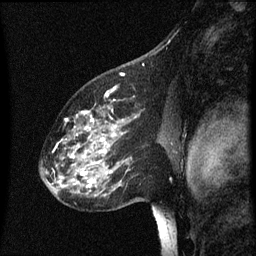
Breast MRI (dynamic contrast-enhanced), one sagittal slice. Position 41 of 60 along the scan axis. Dynamic contrast-enhanced series, image 2 of 3 at this slice position (ordered by acquisition). 1.5 T. TE 4.2 ms, TR 8 ms. 2 mm slice thickness. 256 × 256 image matrix, field of view 200 × 200 mm. Female patient, age 60 years.
Annotated regions visible in this slice (semi-automatic segmentation, software-assisted and operator-edited):
- analysis volume of interest (the breast-tissue region the enhancement analysis was run in; not a lesion): bounding box <49,96,142,197> (left, top, right, bottom; pixels)
- tumour enhancement mask (voxels above the 70 % enhancement threshold inside the analysis volume of interest): <57,112,119,189>